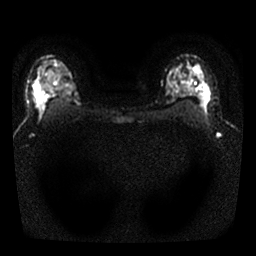
Breast MRI, one axial slice. Slice 19 of 25 in the series (ordered by position). Diffusion-weighted series; image 2 of 4 stored at this slice position (different b-values; order by instance number). 1.5 T. 4 mm slice thickness. 256 × 256 image matrix, field of view 300 × 300 mm. Female patient.
Structures marked on this image (expert manual segmentation):
- tumour on diffusion-weighted imaging: bounding box <35,85,46,106> (left, top, right, bottom; pixels)